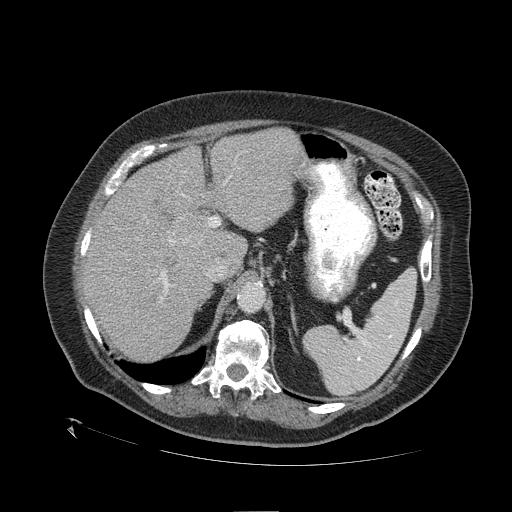
Contrast-enhanced abdominal CT (liver protocol), one axial slice; slice 74 of 109 in the series (ordered by position); reconstruction kernel STANDARD; one of 2 acquisitions stored at this slice position; soft-tissue window (W 400 / L 40 HU); 2.5 mm slice thickness; 512 × 512 image matrix, field of view 460 × 460 mm. Case-level facts recorded for this patient, not image findings: diagnosis: hepatocellular carcinoma (patient treated with transarterial chemoembolisation; whether this scan precedes or follows treatment is not stated here); TNM stage (as recorded): Stage-I; Child-Pugh class: A; tumour differentiation: no biopsy; tumour nodularity: uninodular.
Outlined on this slice (semi-automatically segmented with operator editing):
- liver parenchyma outside the tumour (the mass and vessels are separate outlines, so this box may not span the whole liver): bounding box [x1, y1, x2, y2] px = [82, 128, 302, 360]
- mass: [175, 213, 207, 248]
- liver vessels: [160, 176, 231, 299]